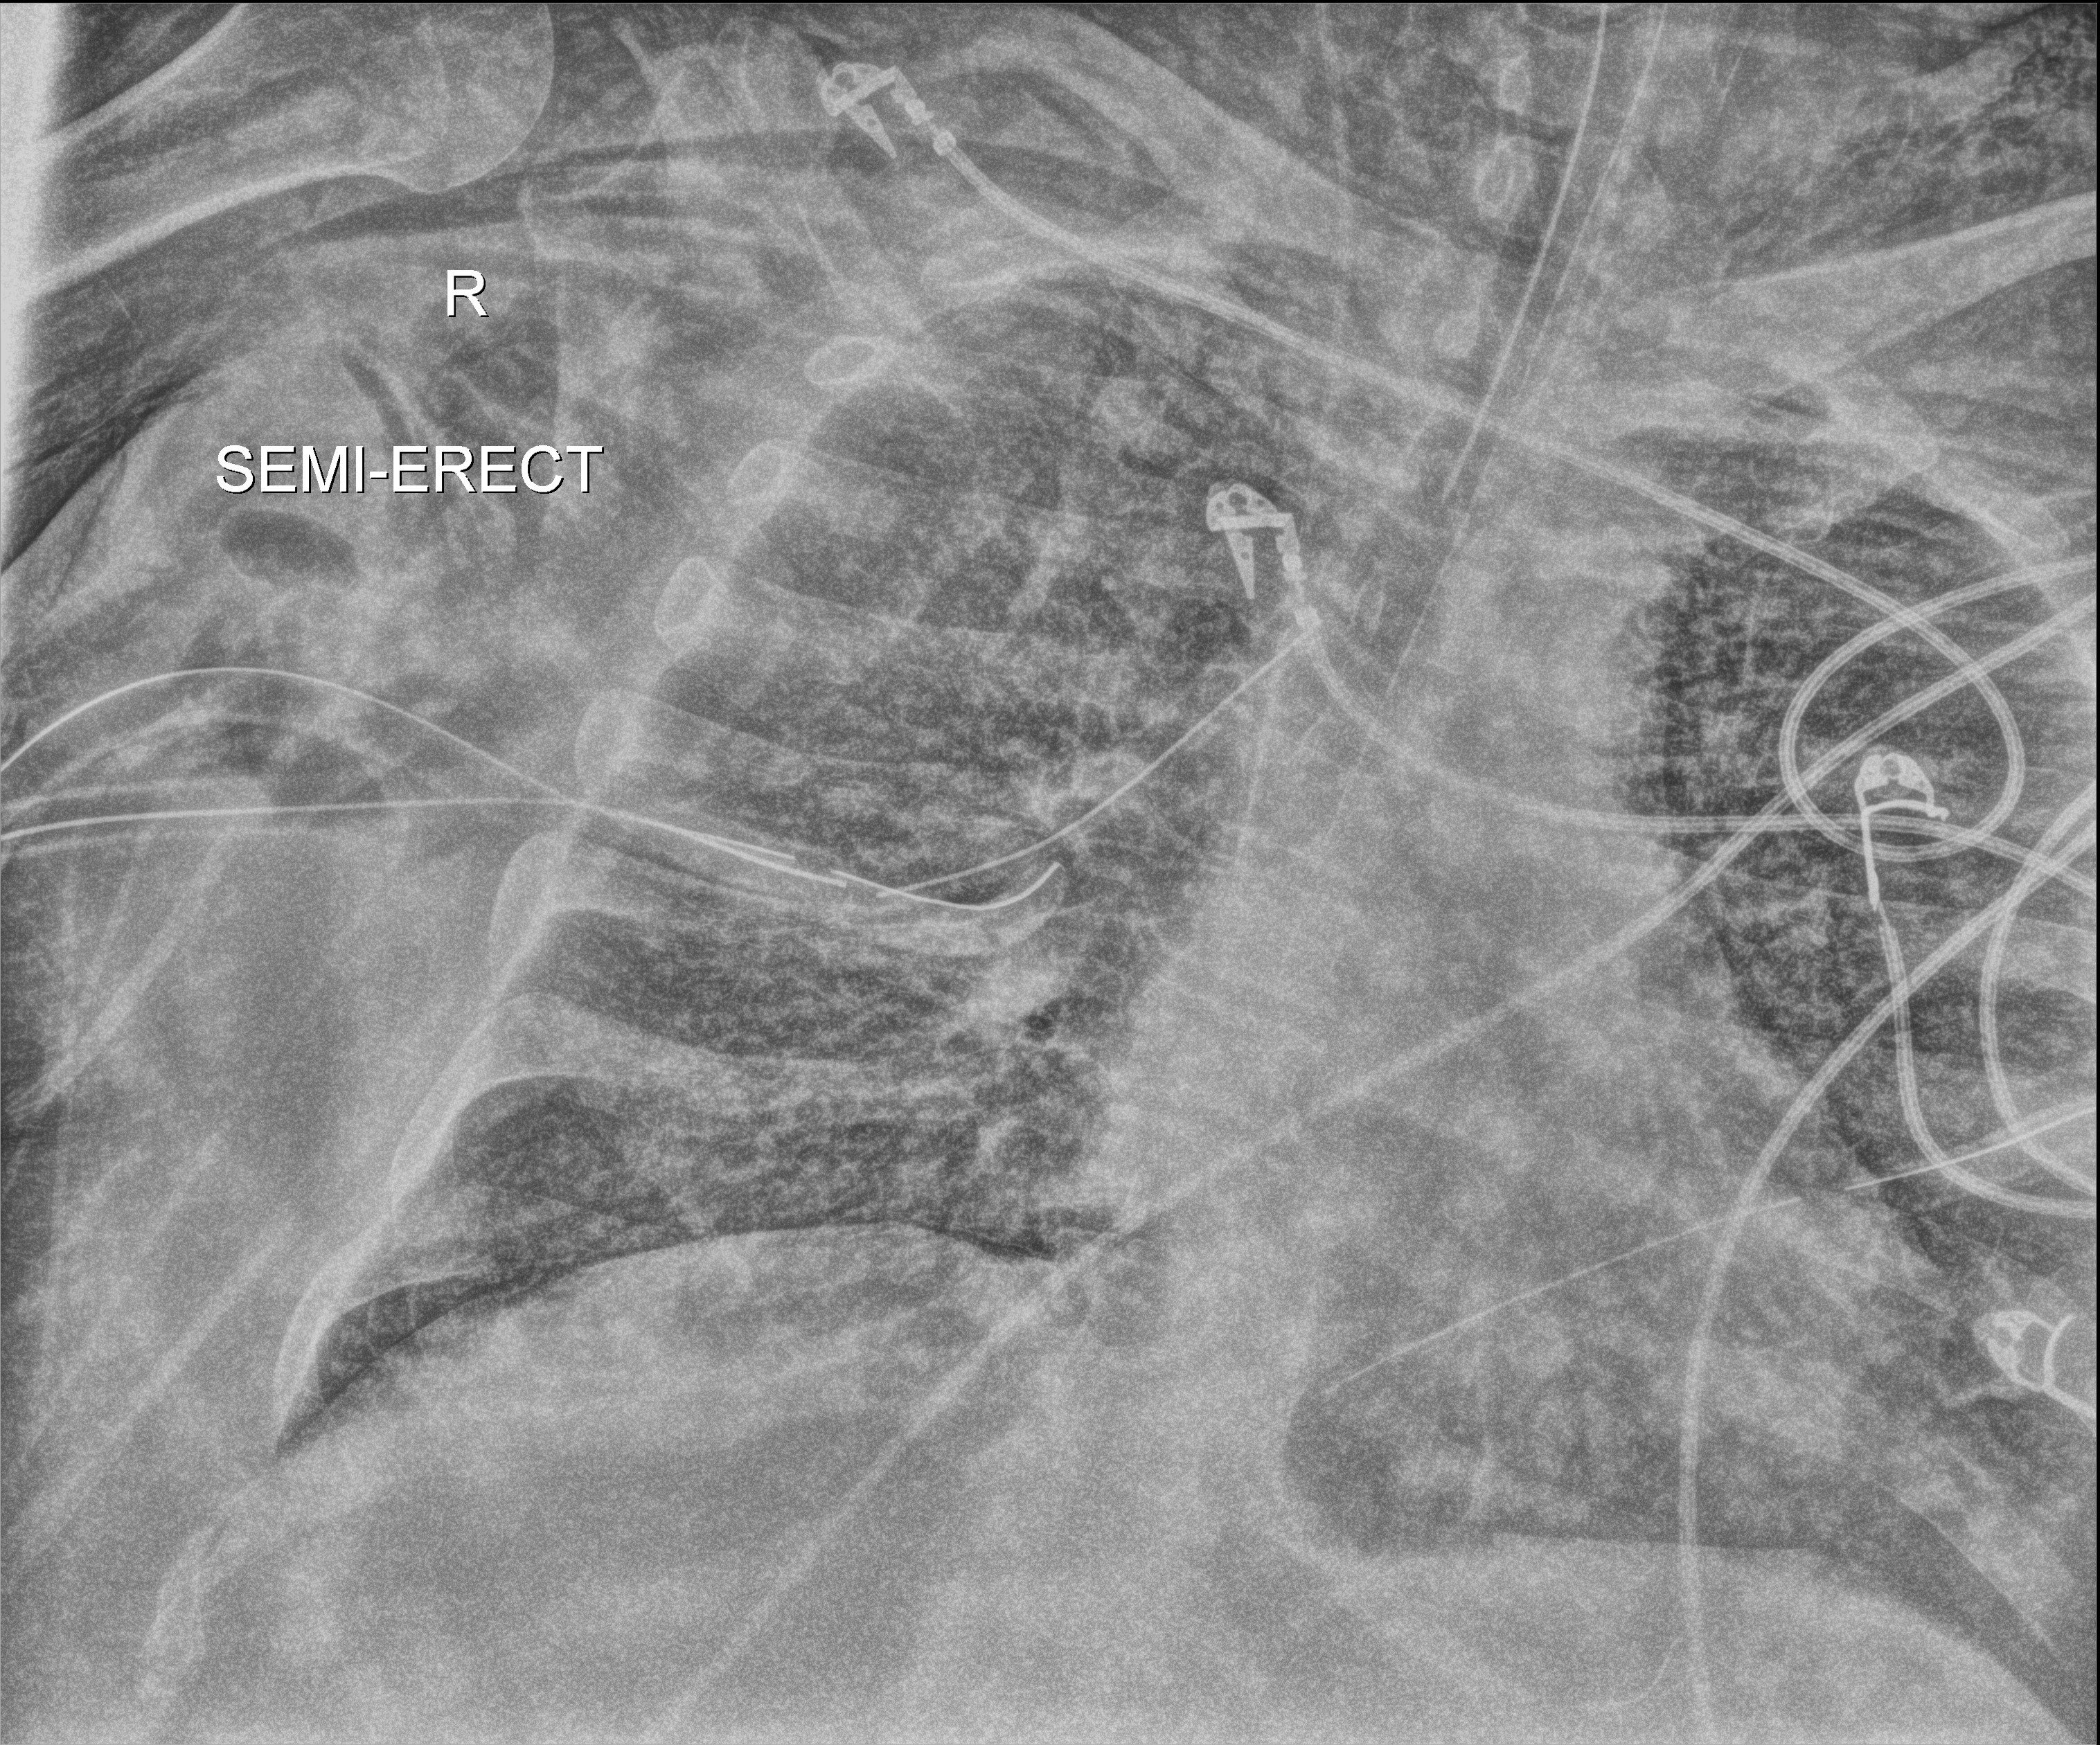
Chest X-ray (portable); anteroposterior (AP) projection. Adult patient hospitalised with COVID-19, age 18–59 years.
From the hospital-stay record, not from the radiograph (when in the stay this image was taken is not recorded):
- hypertension (admission record): yes